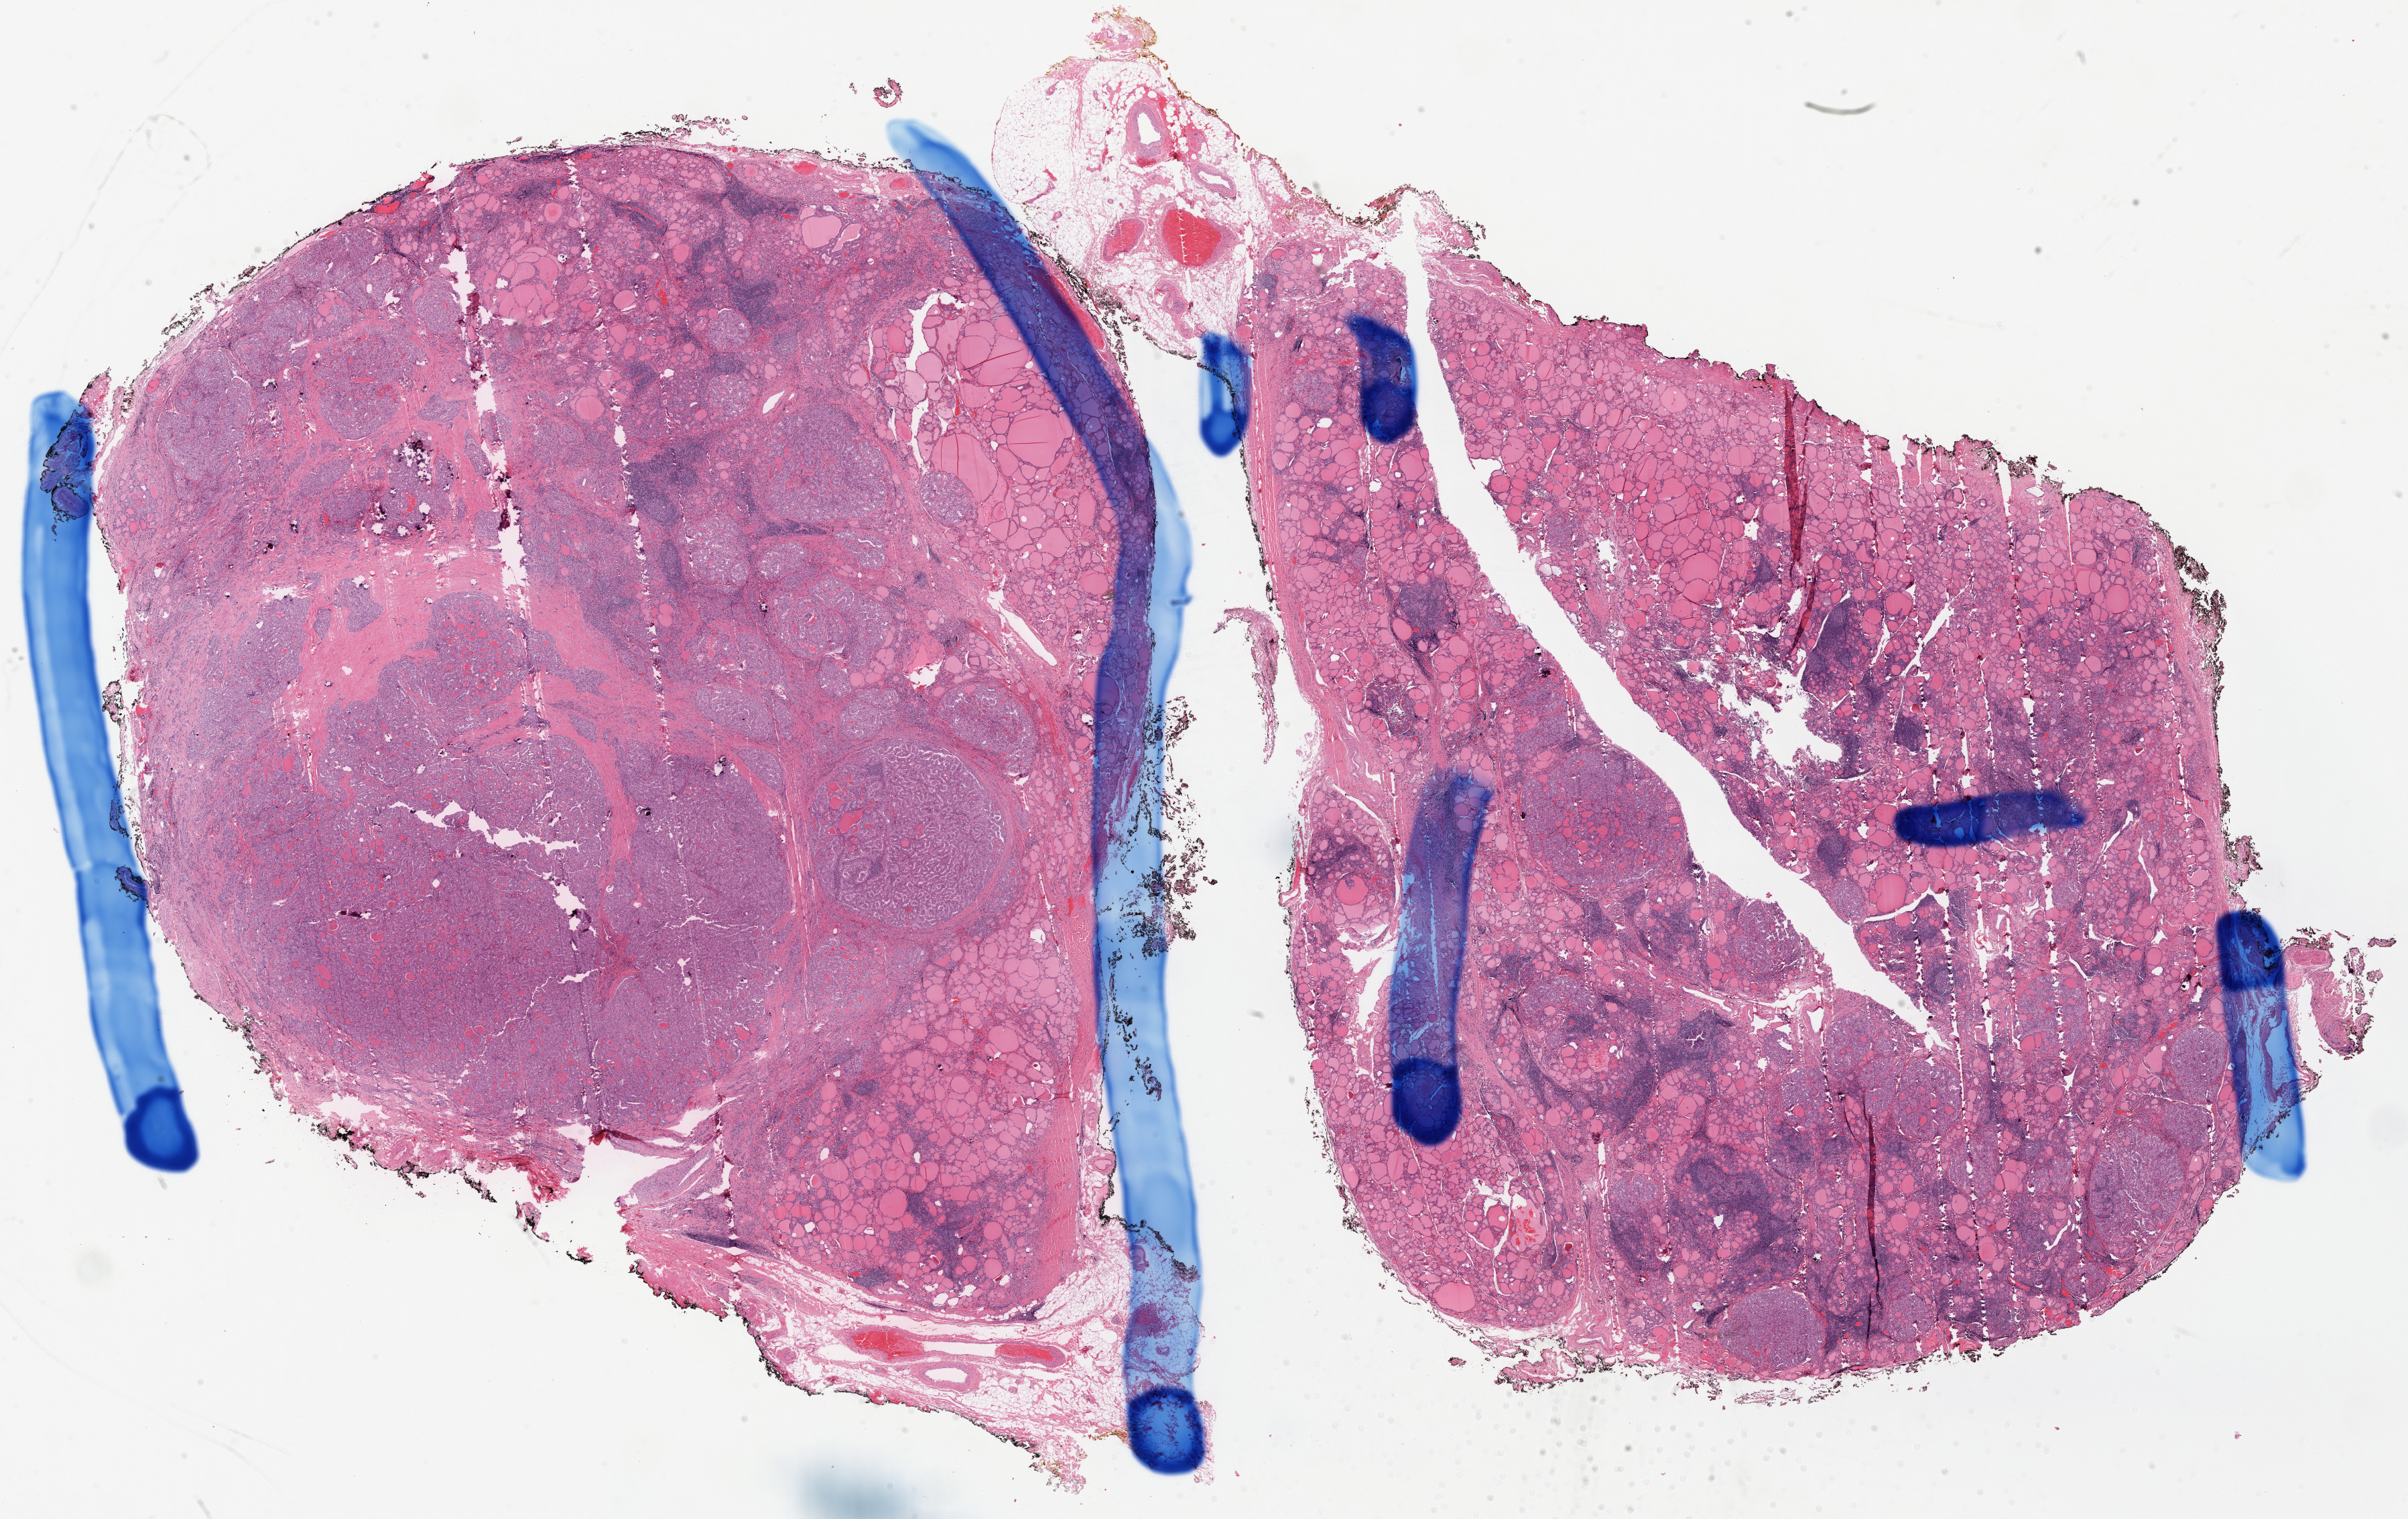
Digitized H&E tissue section (whole slide) — whole scanned area (about 29.0 x 18.3 mm, slide scanned at 40x) shown as a low-resolution overview, formalin-fixed paraffin-embedded (FFPE) diagnostic section, thyroid, primary tumour sample. Female, age 57 years at initial diagnosis.
* TNM: T2 N1b MX
* AJCC pathologic stage: IVA (7th edition)
* diagnosis: Papillary adenocarcinoma, NOS (thyroid gland)